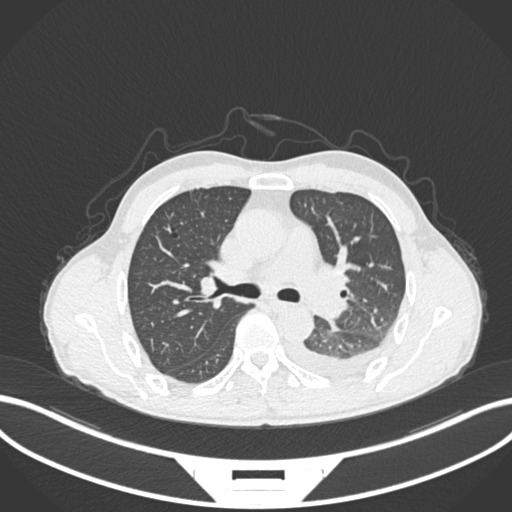
Chest CT, one axial slice. Reconstruction kernel B30f. Lung window (W 1500 / L -600 HU). 512 × 512 image matrix. Patient: male, 47 years. Case-level facts recorded for this patient, not image findings: clinical TNM (as recorded): T3 N1 M1c.
Outlined on this slice (bounding box drawn by a radiologist):
- lung tumour (recorded histology: small cell carcinoma): bounding box <310,292,345,320> (left, top, right, bottom; pixels)